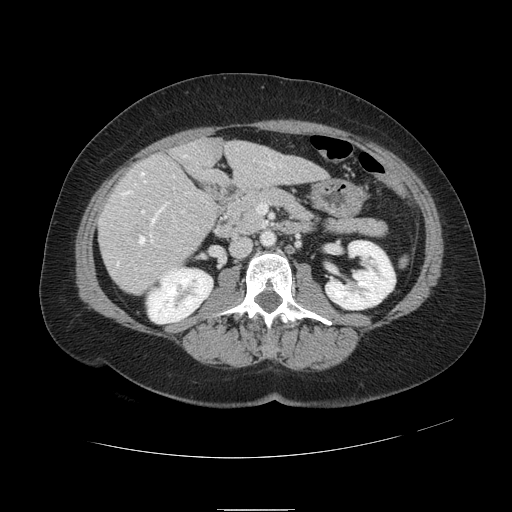
Contrast-enhanced abdominal CT, one axial slice. Position 36 of 121 along the scan axis. 120 kVp. Intravenous contrast given. Soft-tissue window (W 400 / L 40 HU). 512 × 512 image matrix, field of view 400 × 400 mm. Female patient, age 52 years. From the clinical record (not read from this slice): diagnosis: colorectal cancer liver metastases, imaged before liver resection; multiple liver metastases: yes; largest metastasis: 6.3 cm; disease in both lobes: no.
Outlined on this slice (expert manual segmentation):
- hepatic veins: box from (x=117, y=155) to (x=274, y=266) px
- liver: (x=100, y=139)–(x=325, y=294)
- planned liver remnant (the part of the liver to remain after resection): (x=175, y=139)–(x=325, y=185)
- portal vein (with intrahepatic branches): (x=142, y=210)–(x=145, y=214)